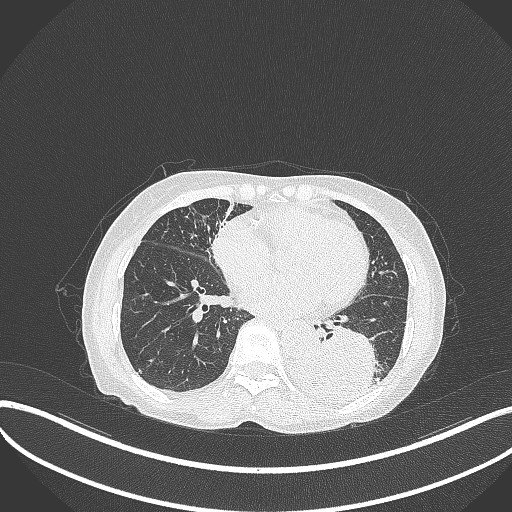
Chest CT, one axial slice. Slice 116 of 370 in the series (ordered by position). Reconstruction kernel B70f. 120 kVp. Lung window (W 1500 / L -600 HU). 1 mm slice thickness. 512 × 512 image matrix, field of view 400 × 400 mm. Female patient, age 78 years. From the clinical record (not read from this slice): clinical TNM (as recorded): T3 N0 M1.
Structures marked on this image (bounding box drawn by a radiologist):
- lung tumour (recorded histology: squamous cell carcinoma): bounding box (x1, y1, x2, y2) in pixels: (286, 324, 380, 408)